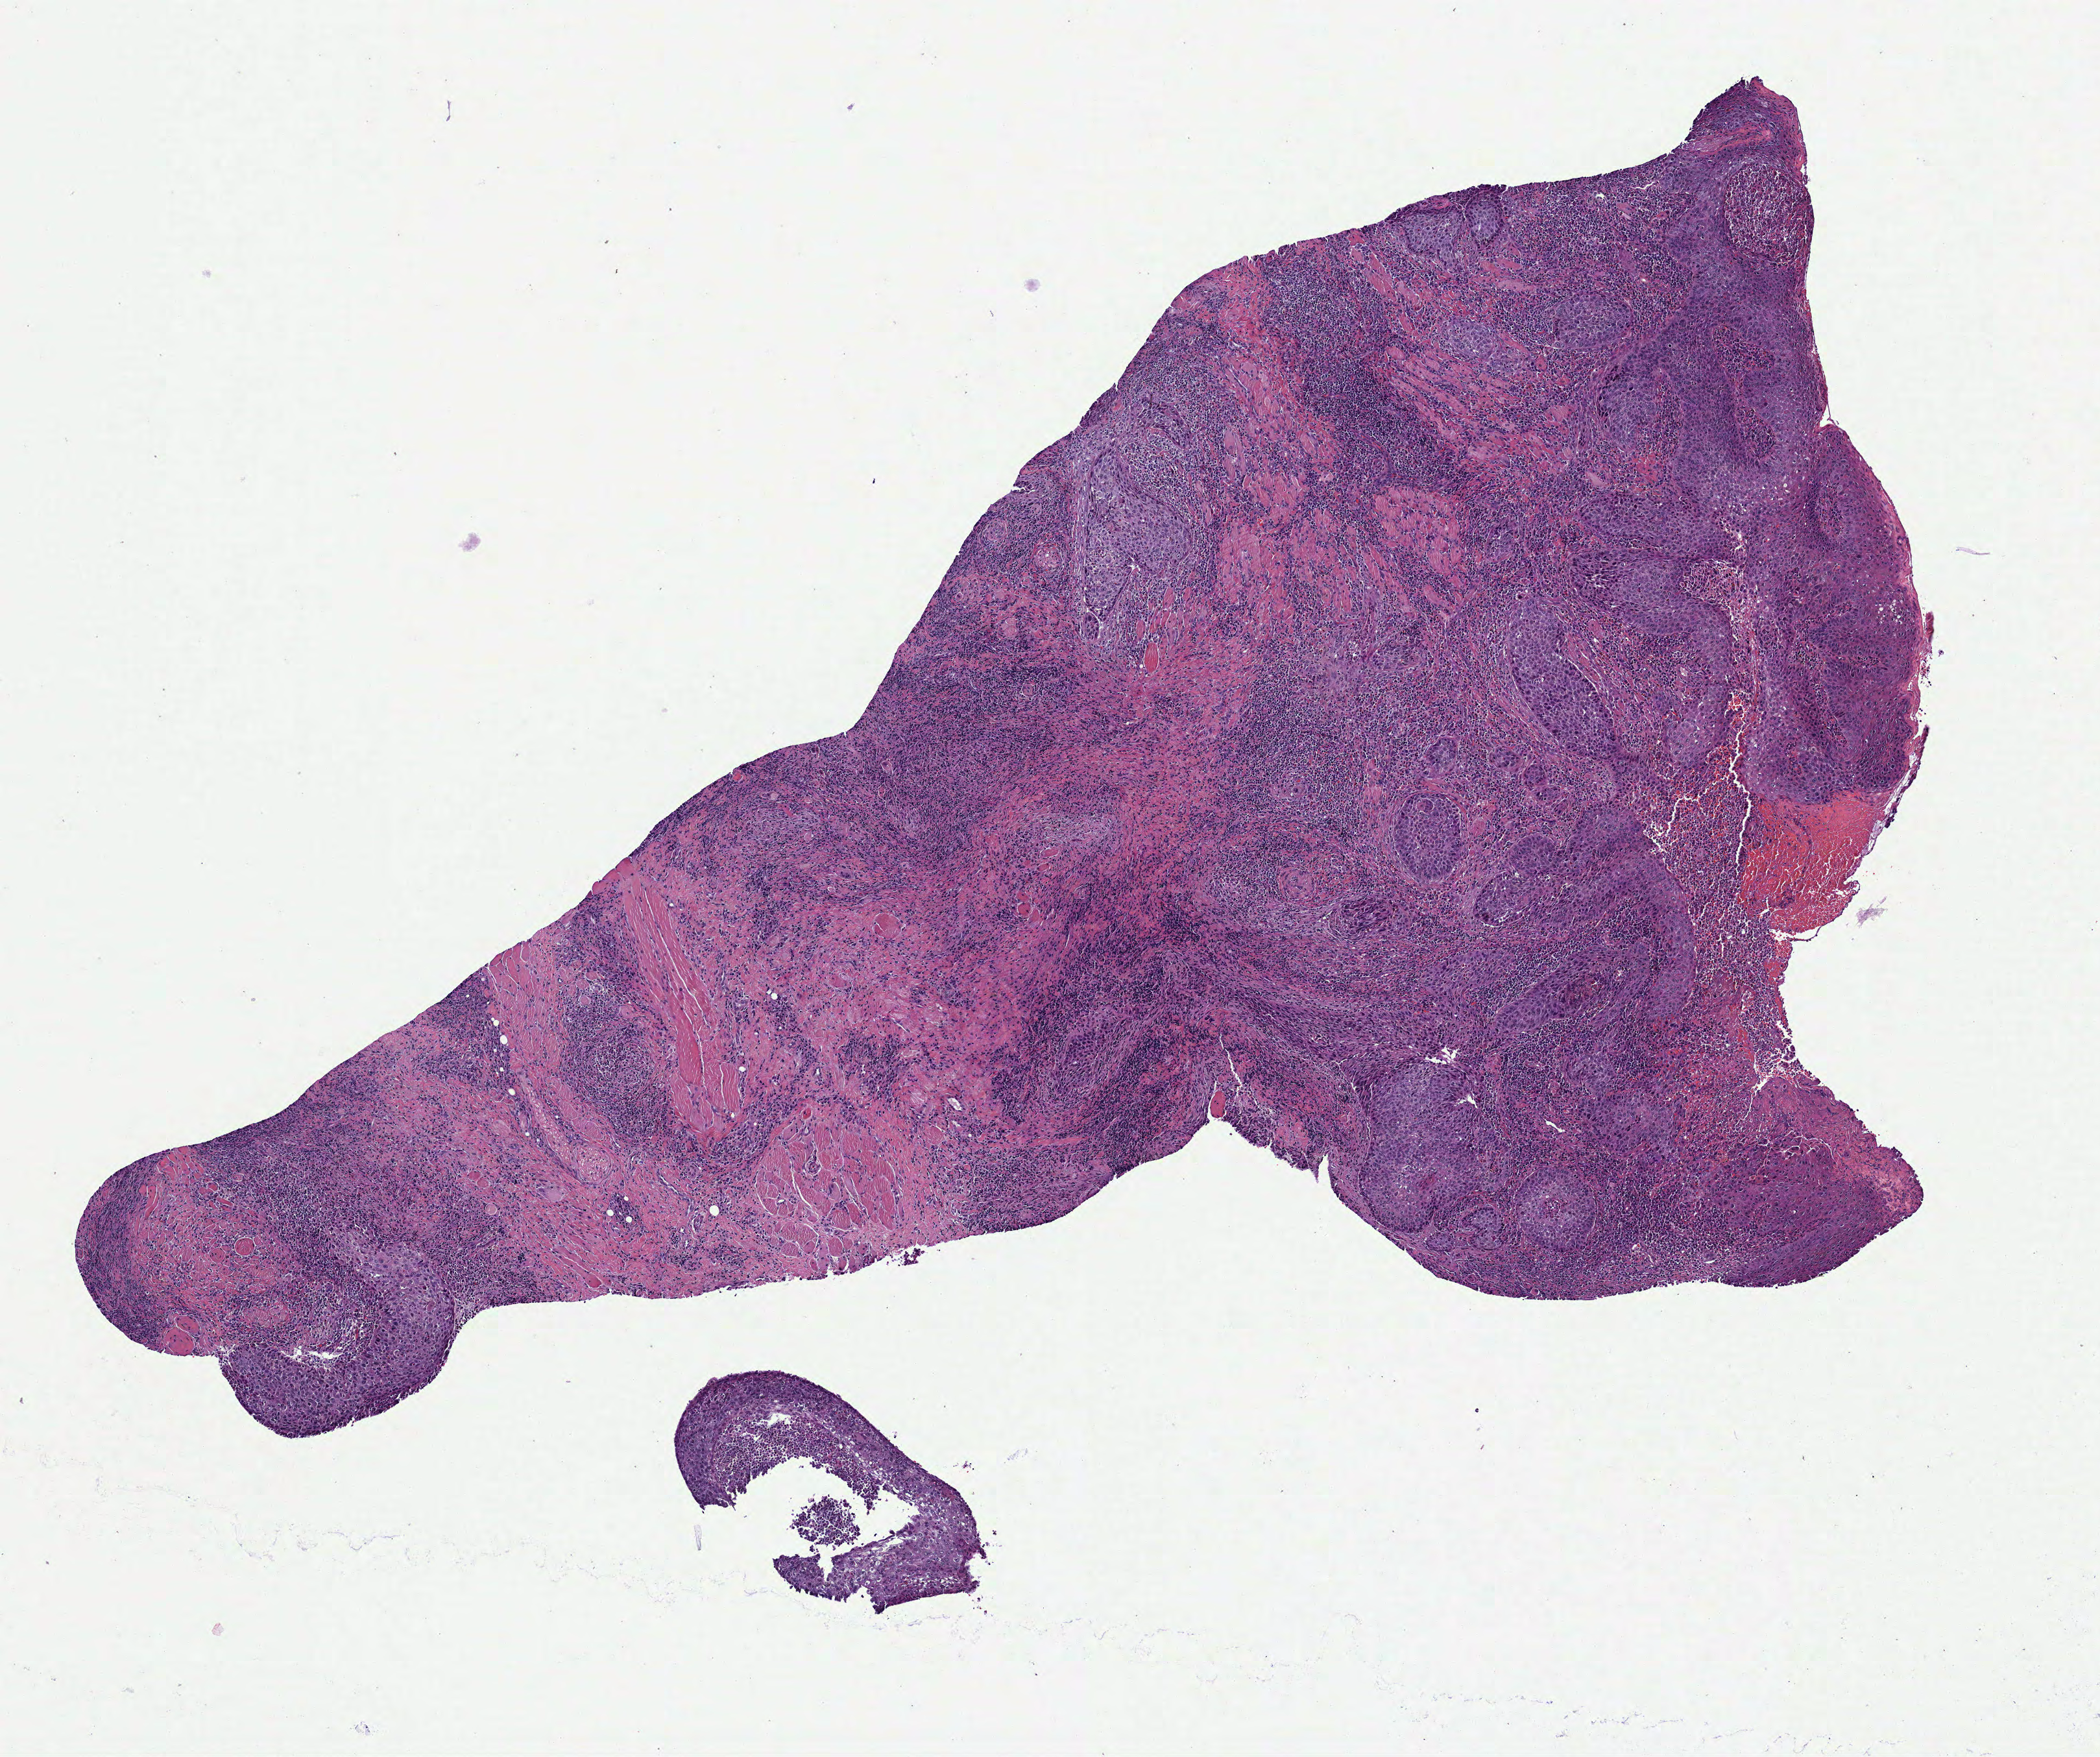
Whole-slide histology image, H&E — low-resolution overview of the scanned area, about 6.5 x 5.5 mm. Formalin-fixed paraffin-embedded (FFPE) diagnostic section. Sample: primary tumour, head and neck. Female, age 79 years at initial diagnosis. Histologic grade: G2 (moderately differentiated).
- laterality: right
- AJCC pathologic stage: III (7th edition)
- diagnosis: Squamous cell carcinoma, NOS